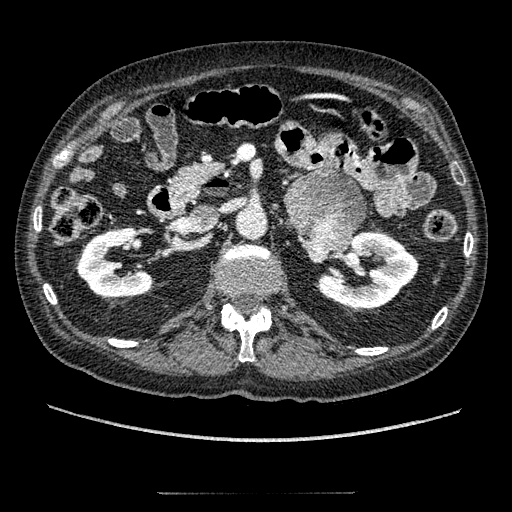
Contrast-enhanced abdominal CT, one axial slice. Position 100 of 274 along the scan axis. 120 kVp. Intravenous contrast given. Soft-tissue window (W 400 / L 40 HU). 512 × 512 image matrix, field of view 381 × 381 mm. Patient: male, 69 years. From the clinical record (not read from this slice): diagnosis: adrenocortical carcinoma; tumour side: left adrenal; tumour size at pathology: 6.1 cm; Ki-67 index: 10 %; stage (as recorded): 3.
Structures marked on this image (semi-automatically segmented with operator editing):
- mass: bounding box <287,171,365,262> (left, top, right, bottom; pixels)